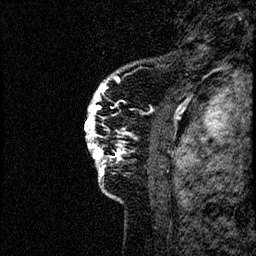
Breast MRI (dynamic contrast-enhanced), one sagittal slice; slice 10 of 60 in the series (ordered by position); dynamic contrast-enhanced study with each time point stored as its own series, time point 2 of 4 at this slice position (early post-contrast, ordered by acquisition time); 1.5 T; TE 4.2 ms, TR 17.6 ms; 2 mm slice thickness; 256 × 256 image matrix, field of view 200 × 200 mm. Patient: female, 40 years. From the clinical record (not read from this slice): setting: breast cancer imaged before/during neoadjuvant chemotherapy; receptor status: HER2-positive.
Annotated regions visible in this slice (semi-automatic segmentation, software-assisted and operator-edited):
- analysis volume of interest (the breast-tissue region the enhancement analysis was run in; not a lesion): bounding box [x1, y1, x2, y2] px = [82, 55, 184, 206]
- tumour enhancement mask (voxels above the 100 % enhancement threshold inside the analysis volume of interest): [85, 83, 121, 174]